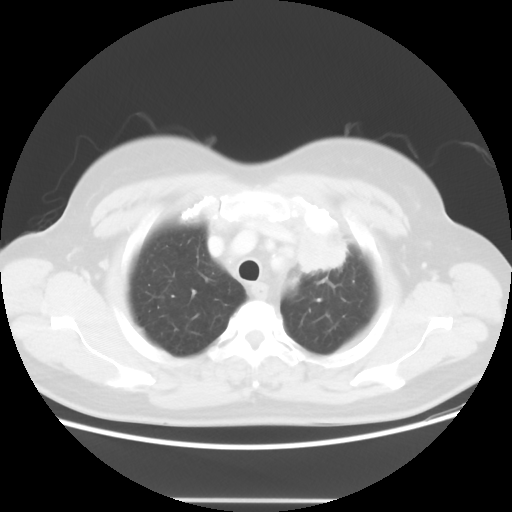
Chest CT, one axial slice; slice 45 of 52 in the series (ordered by position); 120 kVp; lung window (W 1500 / L -600 HU); 5 mm slice thickness; 512 × 512 image matrix. Patient: female, 52 years. Case-level facts recorded for this patient, not image findings: clinical TNM (as recorded): T2 N3 M0.
Structures marked on this image (rectangle marked by the reading radiologist):
- lung tumour (recorded histology: adenocarcinoma): bounding box (x1, y1, x2, y2) in pixels: (292, 220, 355, 277)